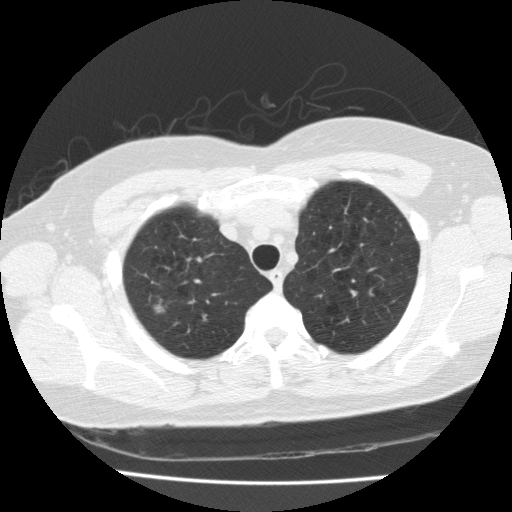
Low-dose screening chest CT, one axial slice. Position 147 of 175 along the scan axis. Reconstruction kernel FC10. 120 kVp. Lung window (W 1500 / L -600 HU). 2 mm slice thickness. 512 × 512 image matrix, field of view 340 × 340 mm.
Outlined on this slice (manually delineated by an expert):
- lesion 1 (tumor, upper lobe of right lung): bounding box <155,304,164,313> (left, top, right, bottom; pixels)